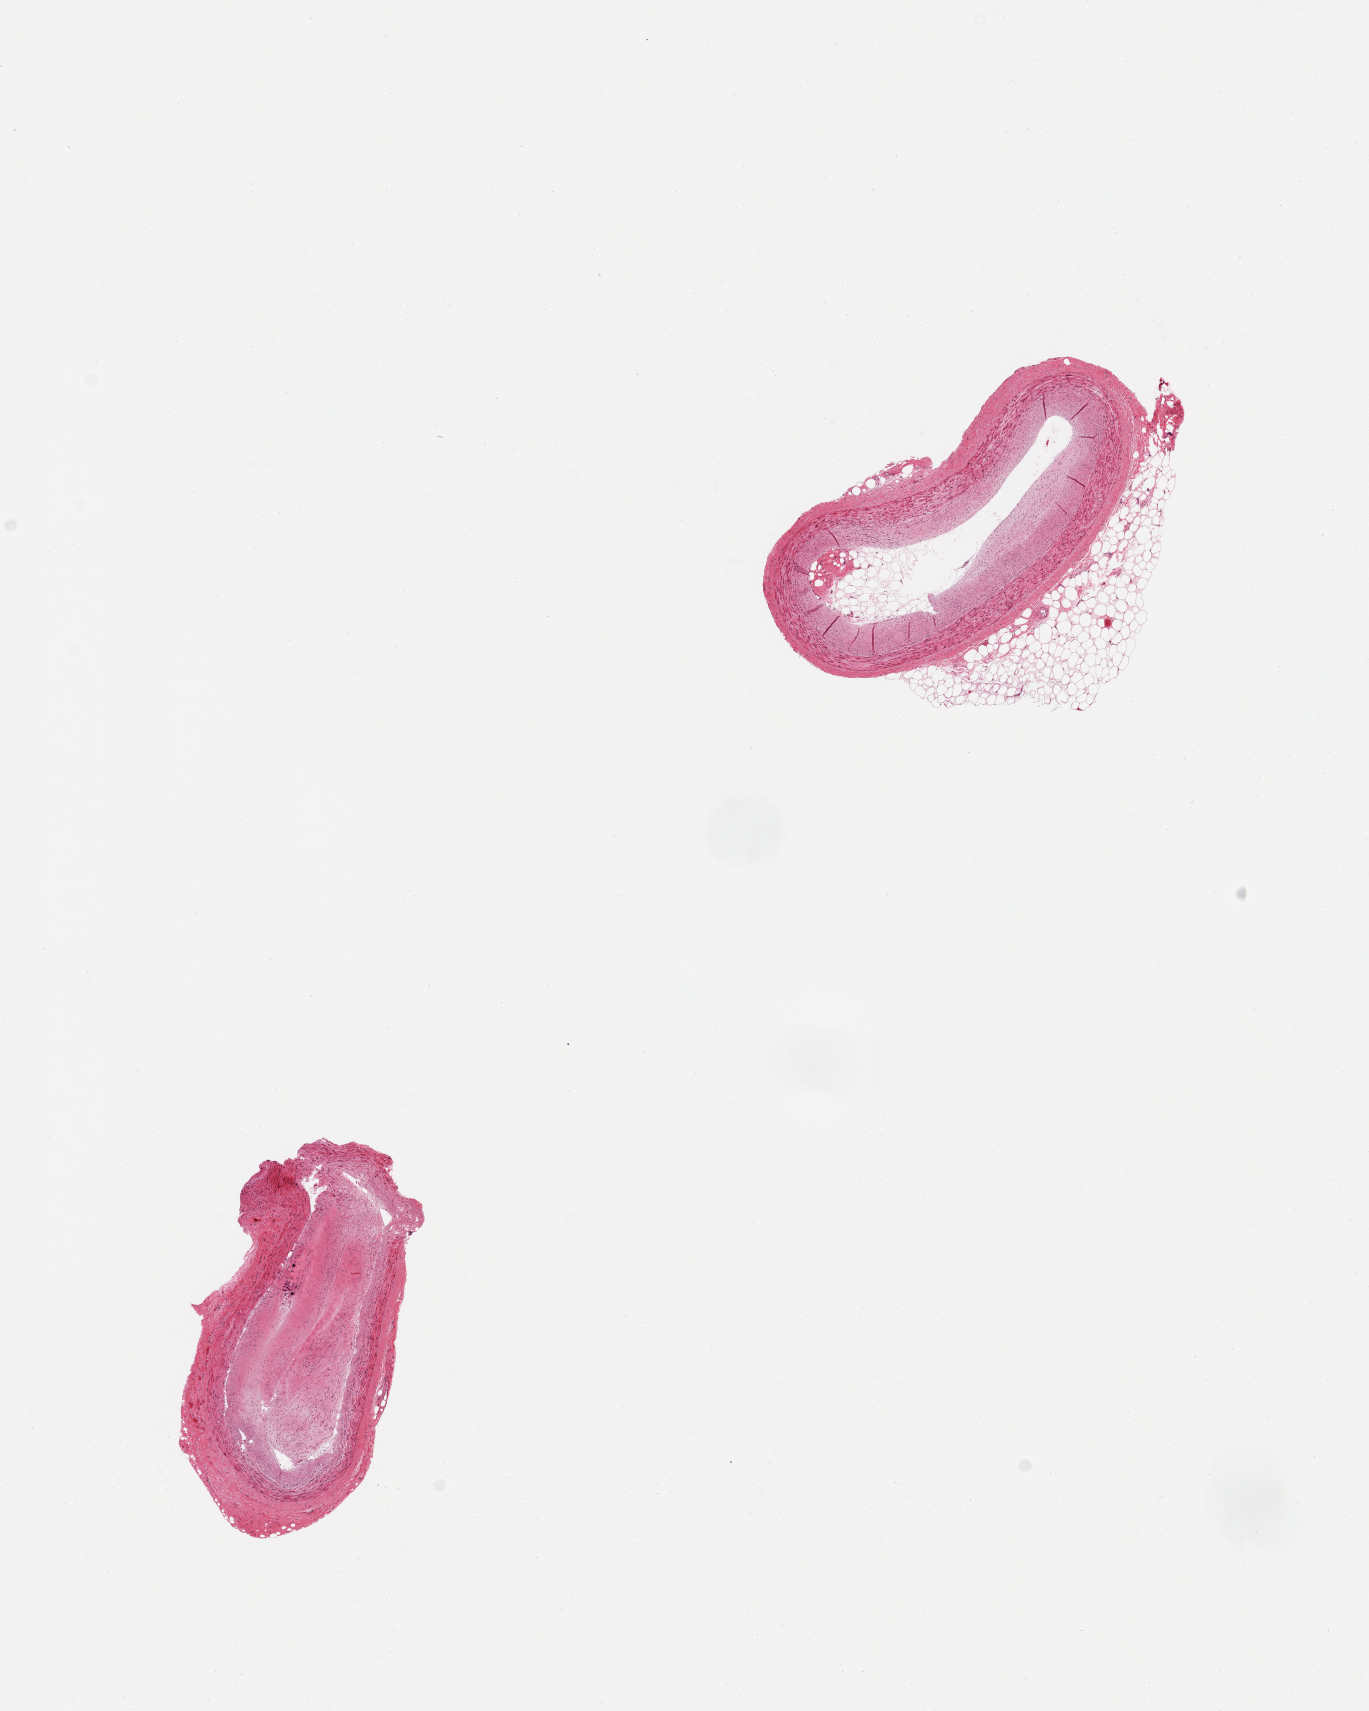
Whole-slide image, H&E stain, a low-resolution overview of the entire scanned area, about 10.8 x 13.5 mm, PAXgene-fixed paraffin-embedded (PFPE) section, sampled site (target tissue): coronary artery, tissue donor sample.
Pathologist's review note for this sample: 2 pieces, small nubbin of fat on one section; atherosclerotic luminal deposits both sections, one totally occclusive.